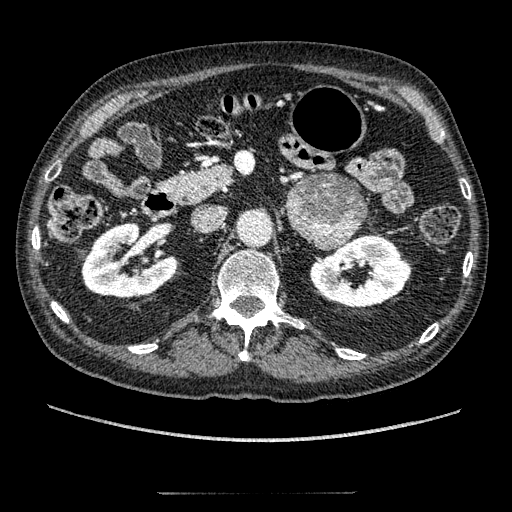
Contrast-enhanced abdominal CT, one axial slice. Slice 110 of 274 in the series (ordered by position). Reconstruction kernel STANDARD. 120 kVp. Intravenous contrast given. Soft-tissue window (W 400 / L 40 HU). 512 × 512 image matrix, field of view 381 × 381 mm. Patient: male, 69 years. From the clinical record (not read from this slice): diagnosis: adrenocortical carcinoma; tumour side: left adrenal; tumour size at pathology: 6.1 cm; Ki-67 index: 10 %; stage (as recorded): 3.
Annotated regions visible in this slice (semi-automatically segmented with operator editing):
- mass: bounding box (x1, y1, x2, y2) in pixels: (290, 176, 365, 247)